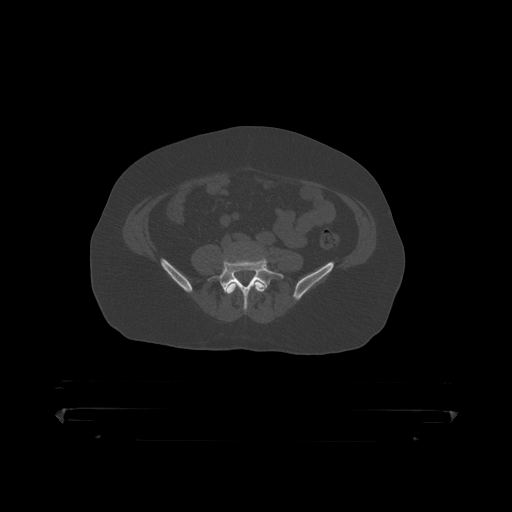
CT including the spine, one axial slice. Position 47 of 390 along the scan axis. Bone window (W 1800 / L 400 HU). 1.25 mm slice thickness. 512 × 512 image matrix, field of view 650 × 650 mm. Male patient, age 60 years. From the clinical record (not read from this slice): primary cancer: prostate.
Structures marked on this image (semi-automatic segmentation, software-assisted and operator-edited):
- L4 vertebra: bounding box (x1, y1, x2, y2) in pixels: (227, 281, 265, 309)
- L5 vertebra: (210, 260, 284, 304)